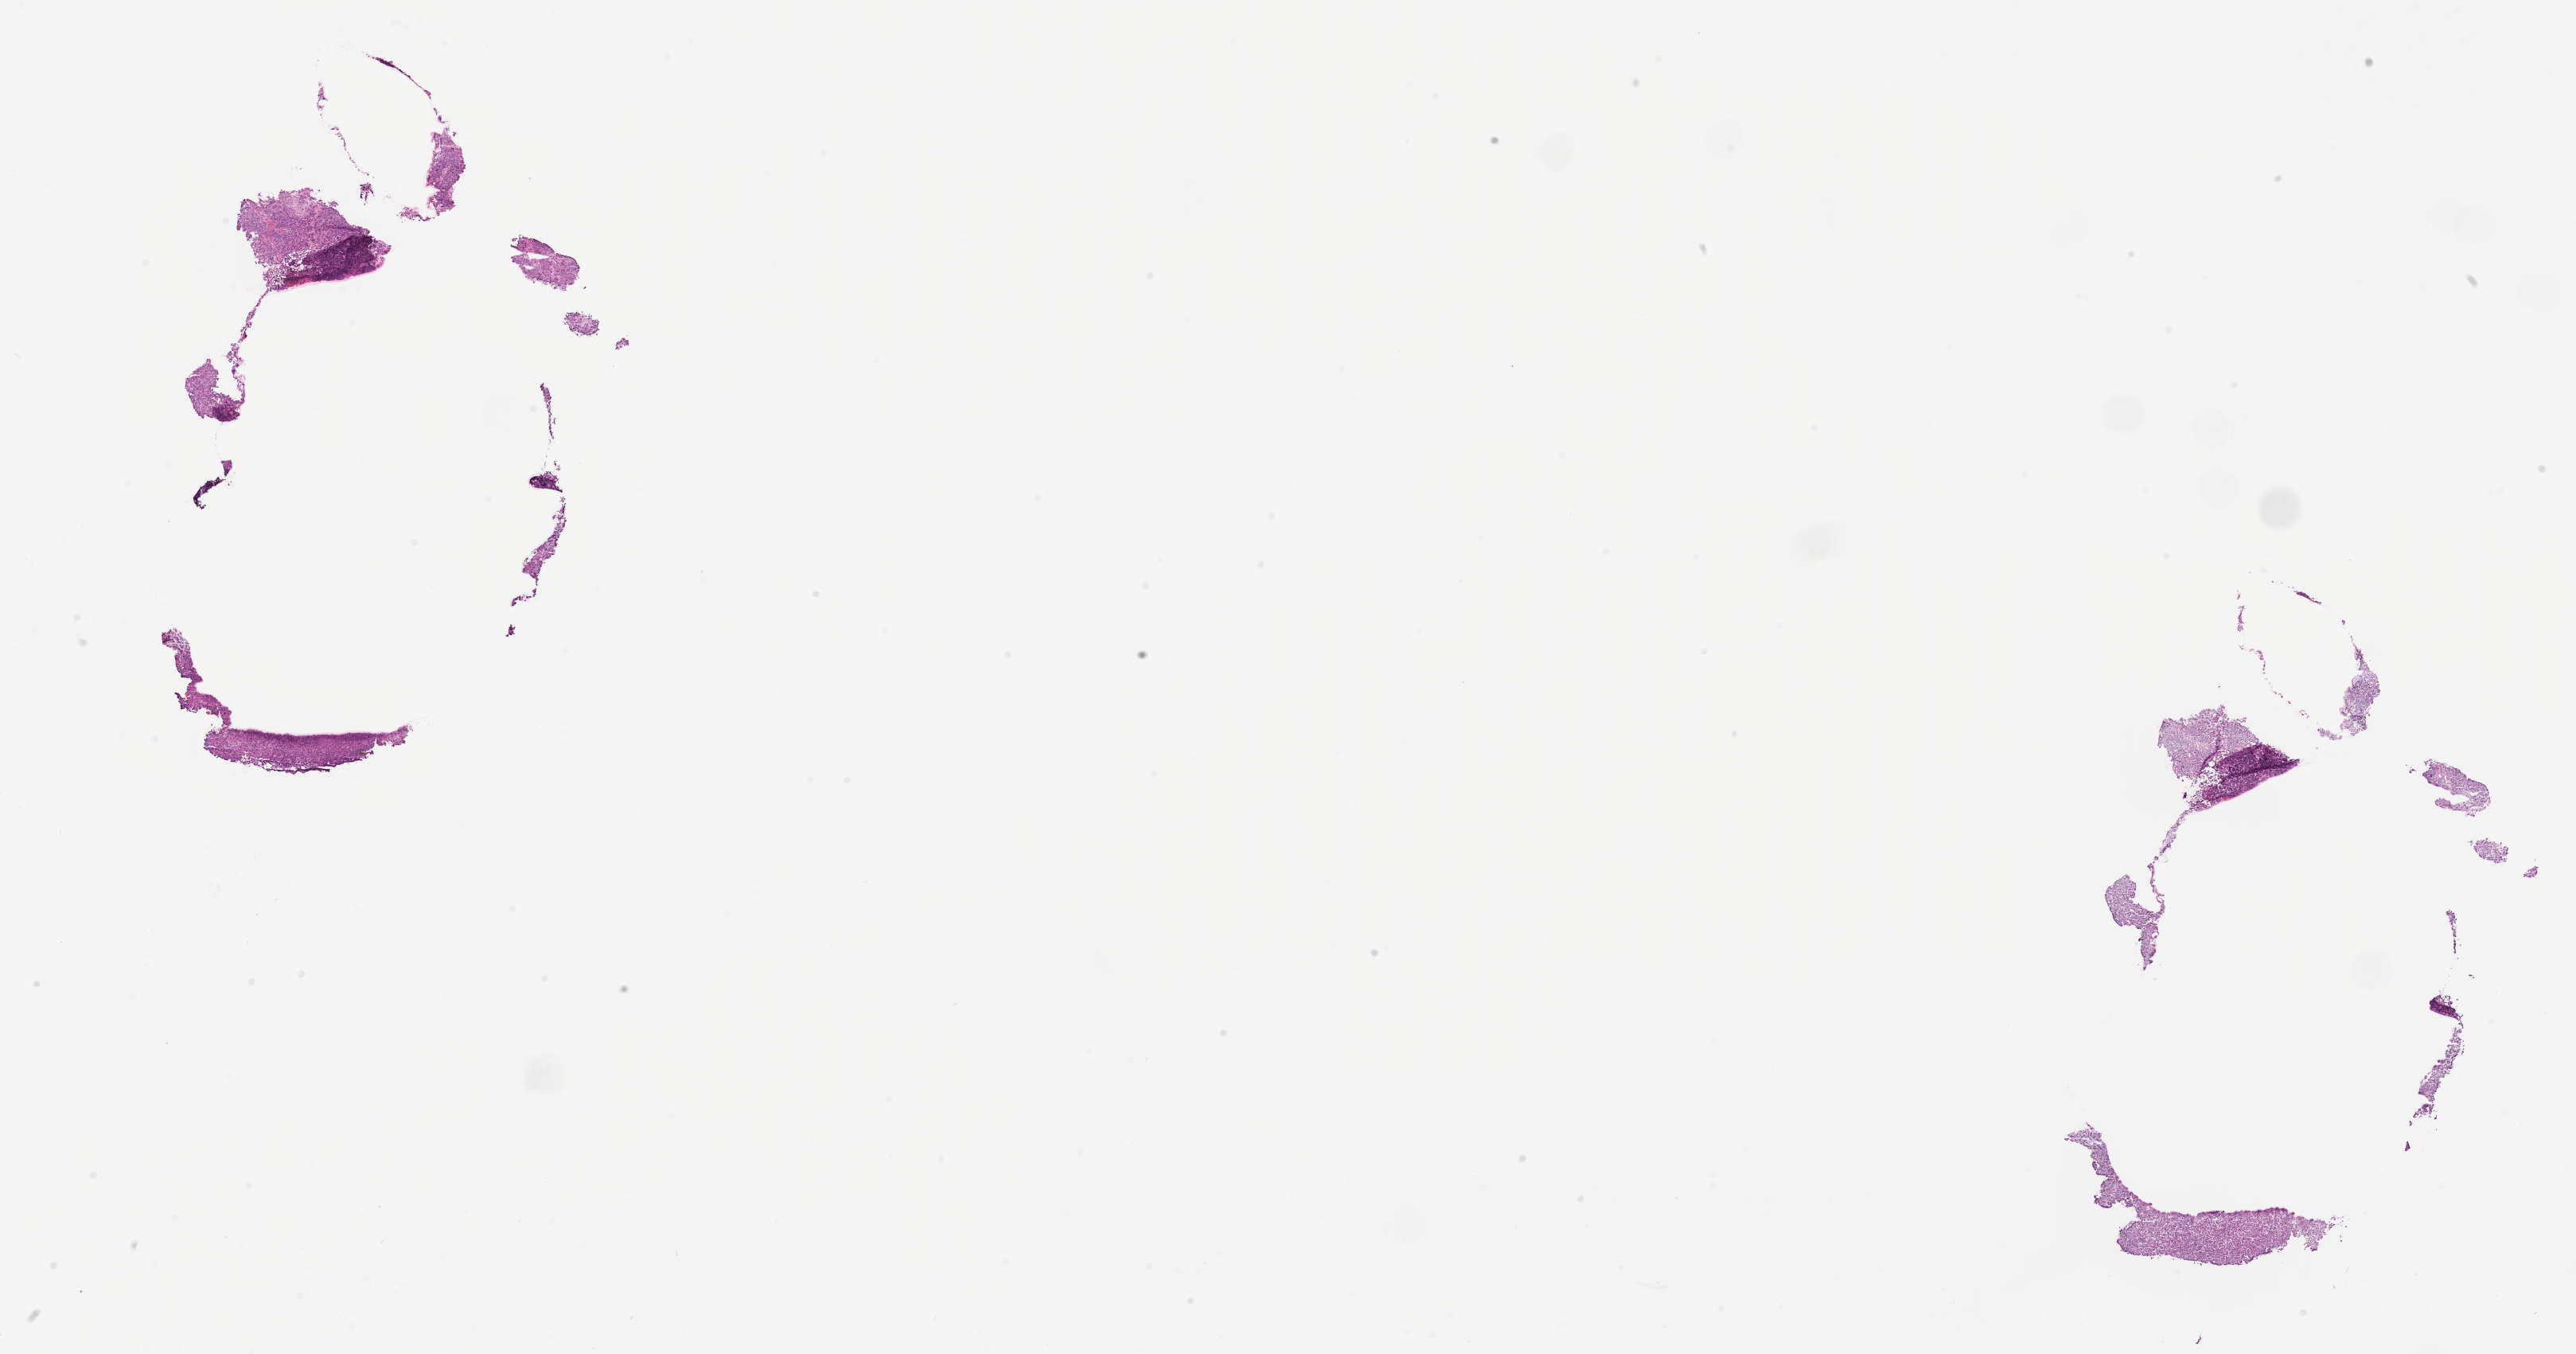
Whole-slide image, hematoxylin and eosin (H&E) stain — whole scanned area (about 26.1 x 13.7 mm) shown as a low-resolution overview, frozen section (tissue freezing medium), specimen: primary tumor, anatomic site: breast. Female, age 38 years at initial diagnosis.
Diagnosis: Infiltrating duct carcinoma, NOS.